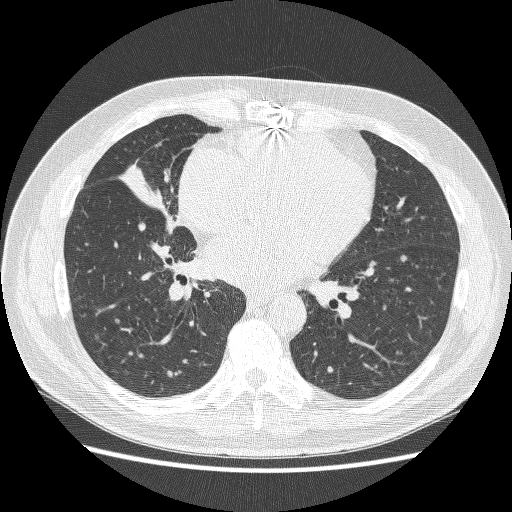
Low-dose screening chest CT, axial slice, first (baseline) screen, lung window (W 1500 / L -600 HU), lung (sharp) reconstruction kernel (BONE), 120 kVp, slice 121 of 251 in the series. Male participant, aged 59 years at enrolment. Former smoker at enrolment.
Expert-annotated lung lesion, bounding box (x1, y1, x2, y2) in pixels: (108, 153, 196, 243). No non-calcified nodule or mass ≥4 mm was recorded by the screening reader at this exam. Participant outcome: lung cancer diagnosed 24 days after this screen — adenocarcinoma, NOS, right middle lobe, poorly differentiated (G3), stage IV (AJCC 6th edition), 54 mm at pathology.